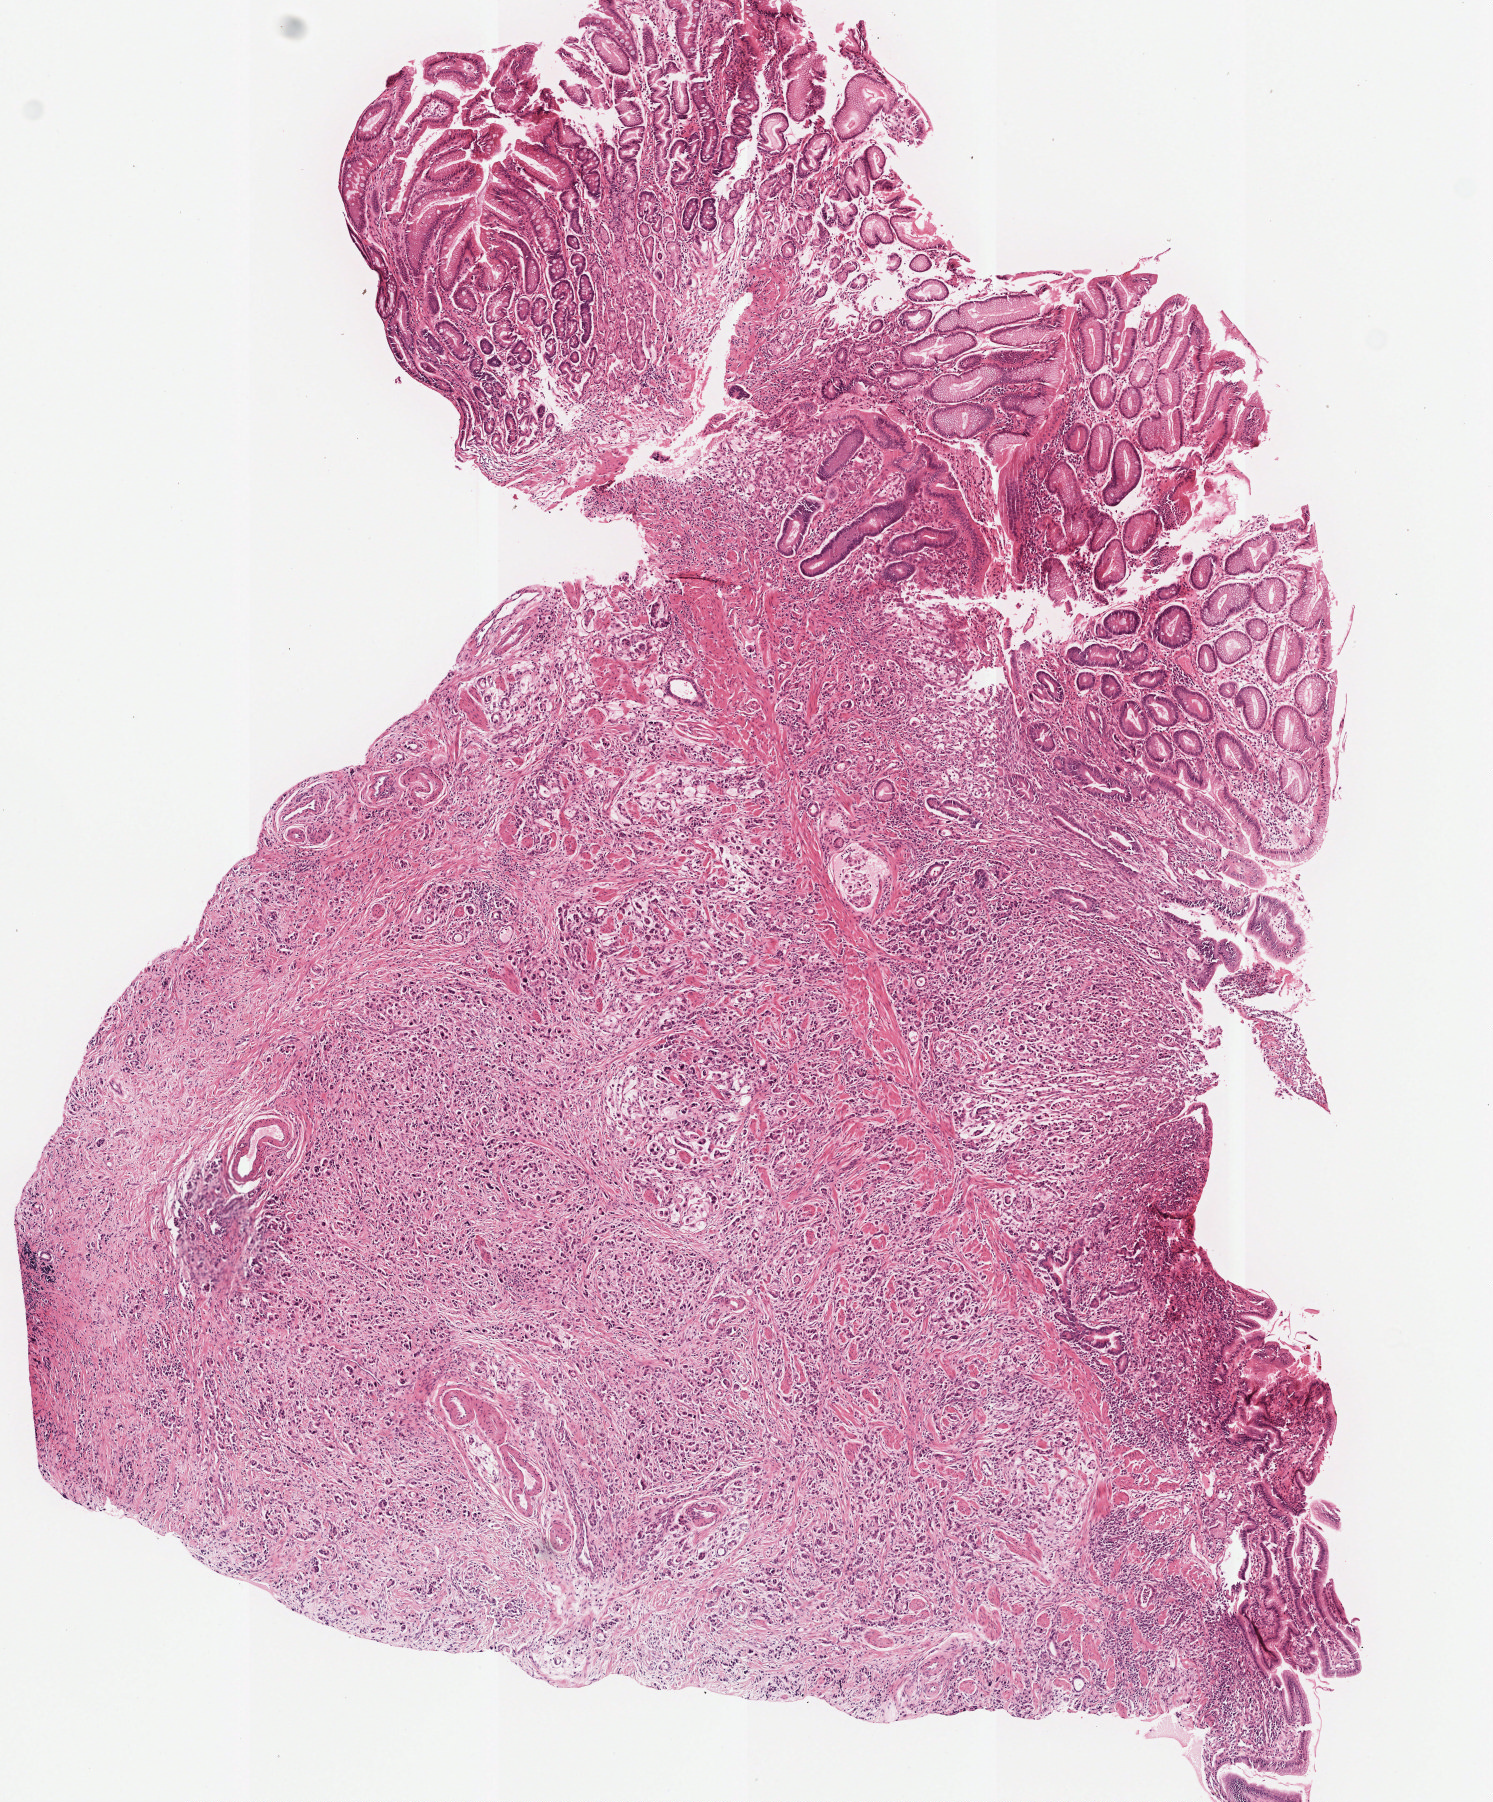
Digitized Hematoxylin and eosin (H&E) stained tissue section (whole slide) — low-resolution overview of the scanned area, about 5.9 x 7.1 mm (acquisition: 20x scan); formalin-fixed paraffin-embedded (FFPE) diagnostic section; primary tumour sample from the stomach. Female, age 76 years at initial diagnosis. Histologic grade: G3 (poorly differentiated).
Lymph nodes positive (case pathology): 1 of 62 examined. AJCC pathologic stage: IIIA (7th edition). Pathologic diagnosis: Carcinoma, diffuse type (gastric antrum).